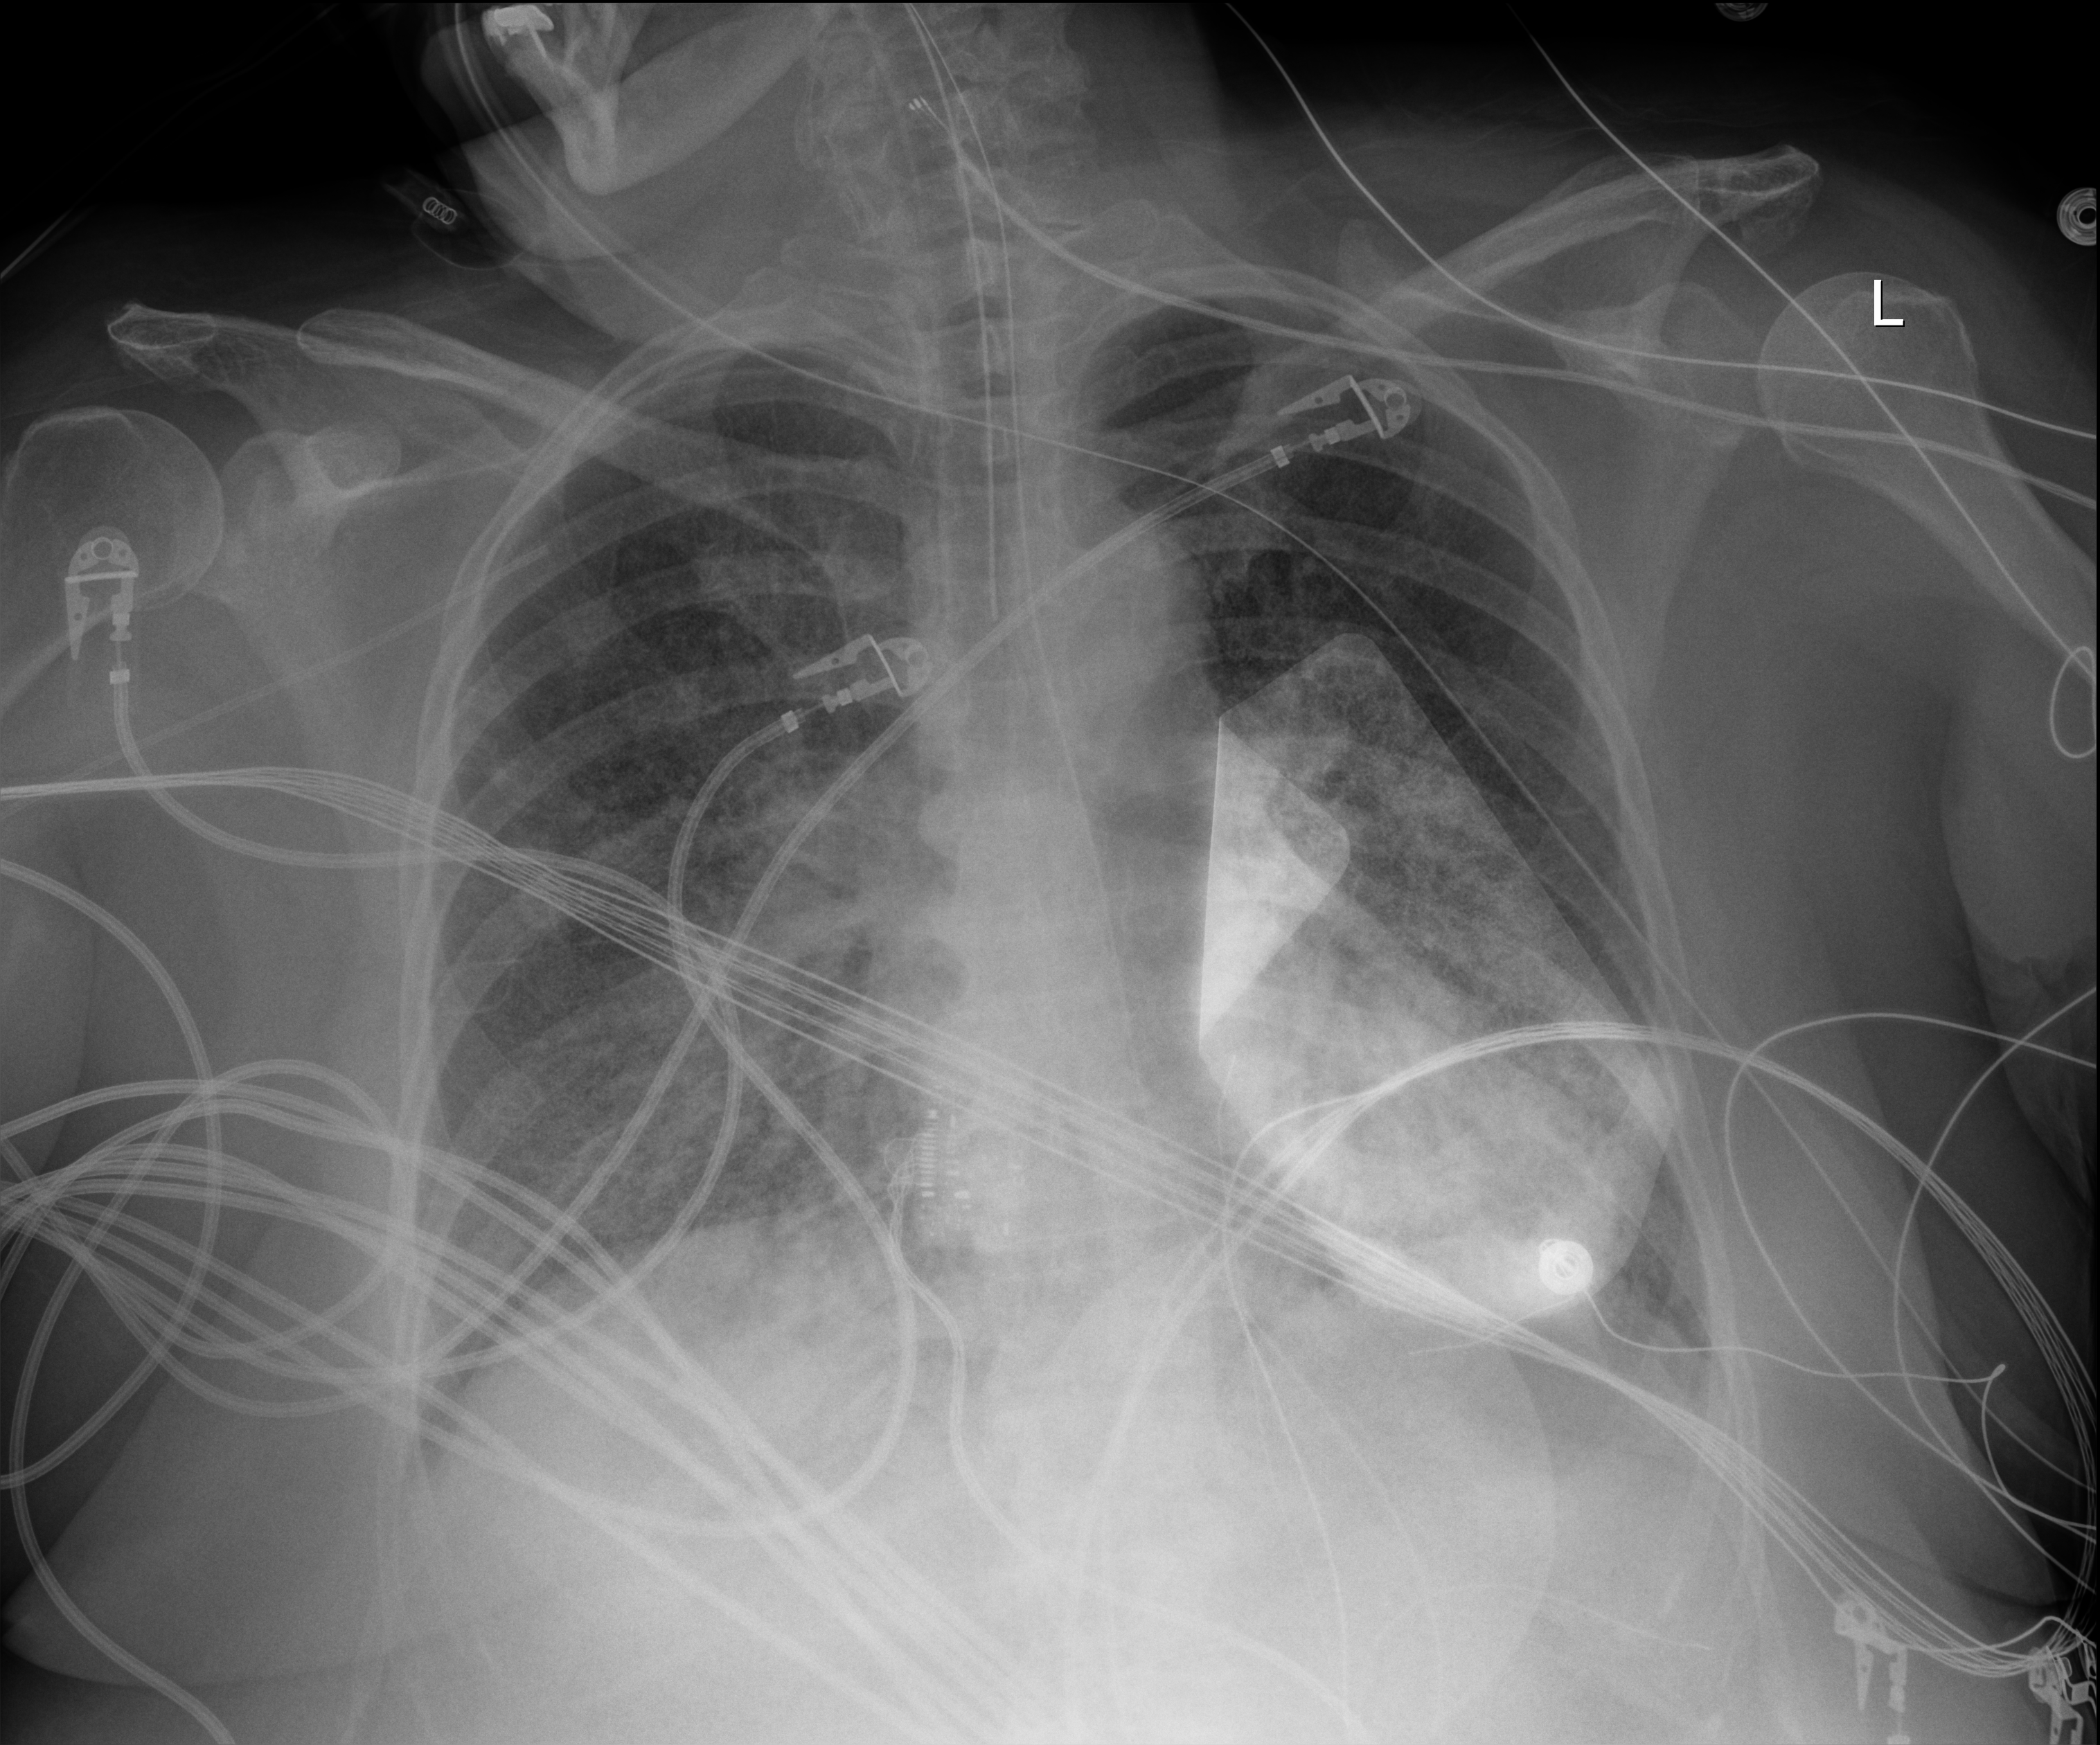
Chest radiograph (digital radiography), anteroposterior (AP) projection. Patient hospitalised with COVID-19; female, aged 60–74 years.
Admission-level facts for this patient (not findings on this image; timing relative to this image not recorded): mechanically ventilated during this hospital stay: yes; admitted to intensive care during this hospital stay: yes; COPD (admission record): no.